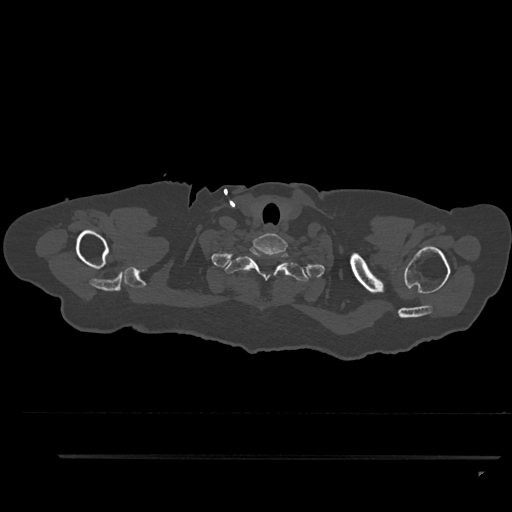
CT including the spine, one axial slice. Position 773 of 797 along the scan axis. 120 kVp. Bone window (W 1800 / L 400 HU). 0.5 mm slice thickness. 512 × 512 image matrix, field of view 408 × 408 mm. Female patient, age 44 years. From the clinical record (not read from this slice): primary cancer: renal; vertebrae with lytic lesions (as recorded): L1.
Outlined on this slice (semi-automatically segmented with operator editing):
- T1 vertebra: box from (x=224, y=246) to (x=309, y=282) px